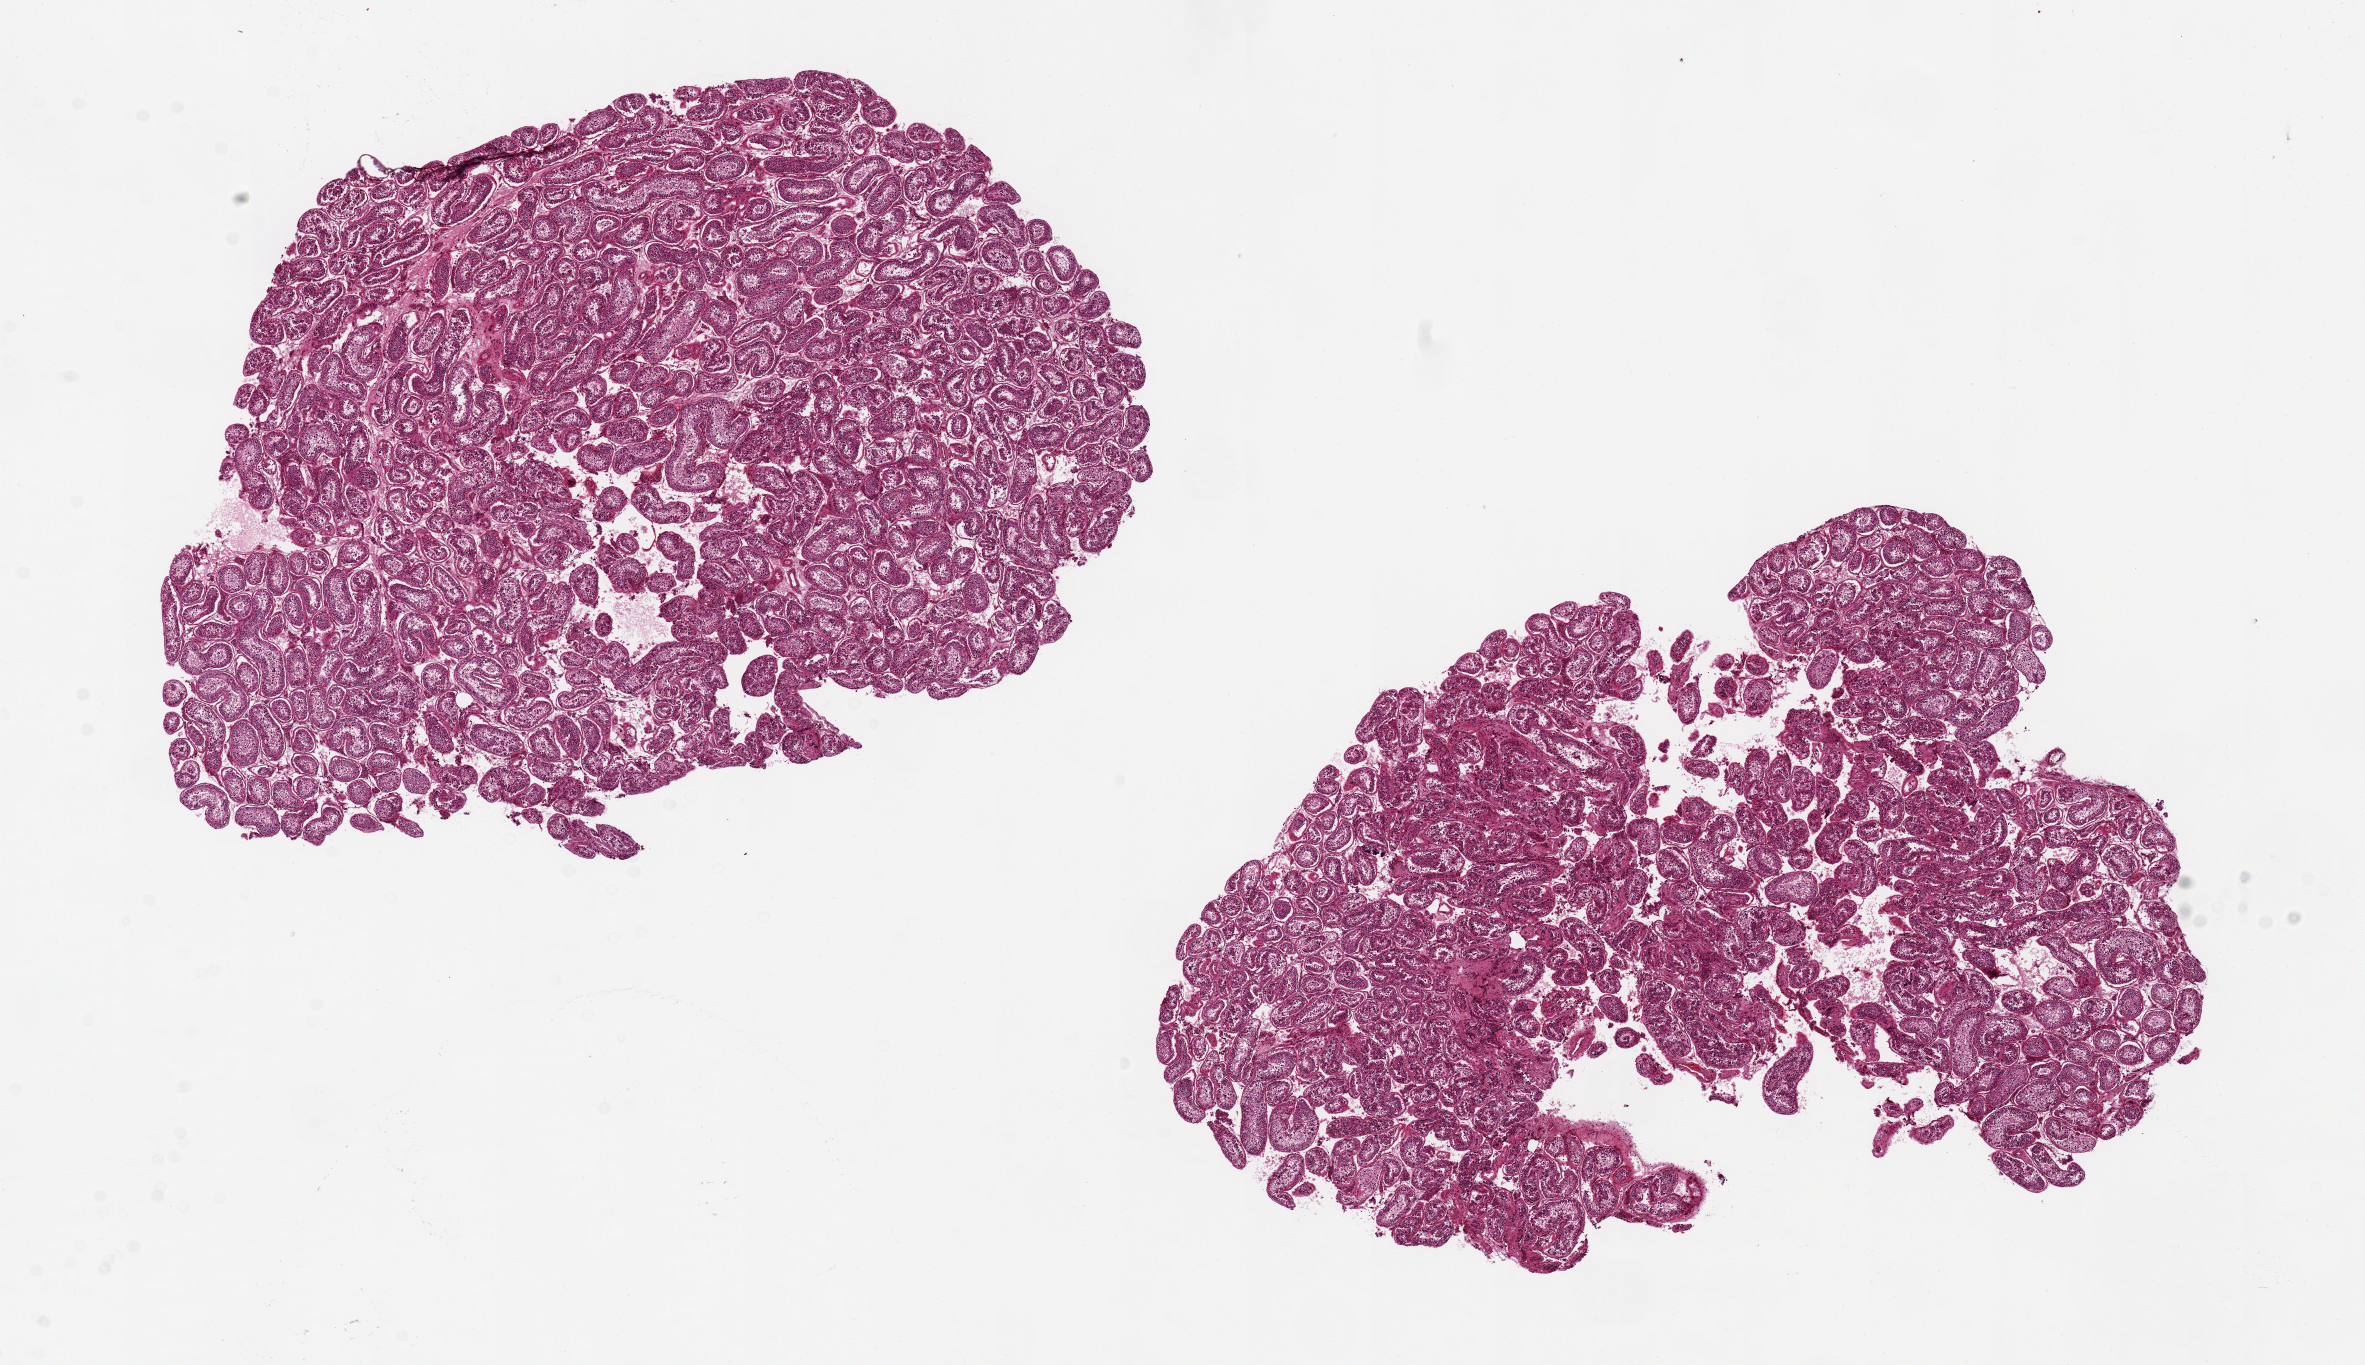
Digitized H&E-stained section, low-resolution overview of the scanned area, about 18.7 x 10.8 mm (acquisition: 20x scan). PAXgene-fixed, paraffin-embedded tissue. Sampled site (target tissue): testis. Tissue donor sample.
Reviewer comment on this tissue sample: 2 aliquots, ~8x5mm. Spermatogenesis visible but appears slightly reduced.